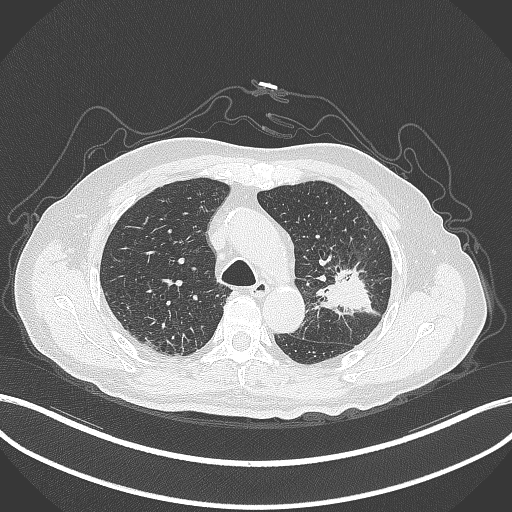
Chest CT, one axial slice; position 206 of 331 along the scan axis; reconstruction kernel B70f; 120 kVp; lung window (W 1500 / L -600 HU); 512 × 512 image matrix, field of view 400 × 400 mm. Patient: male, 79 years. Case-level facts recorded for this patient, not image findings: clinical TNM (as recorded): T2a N1 M1.
Structures marked on this image (bounding box drawn by a radiologist):
- lung tumour (recorded histology: adenocarcinoma): bounding box [x1, y1, x2, y2] px = [315, 261, 380, 317]